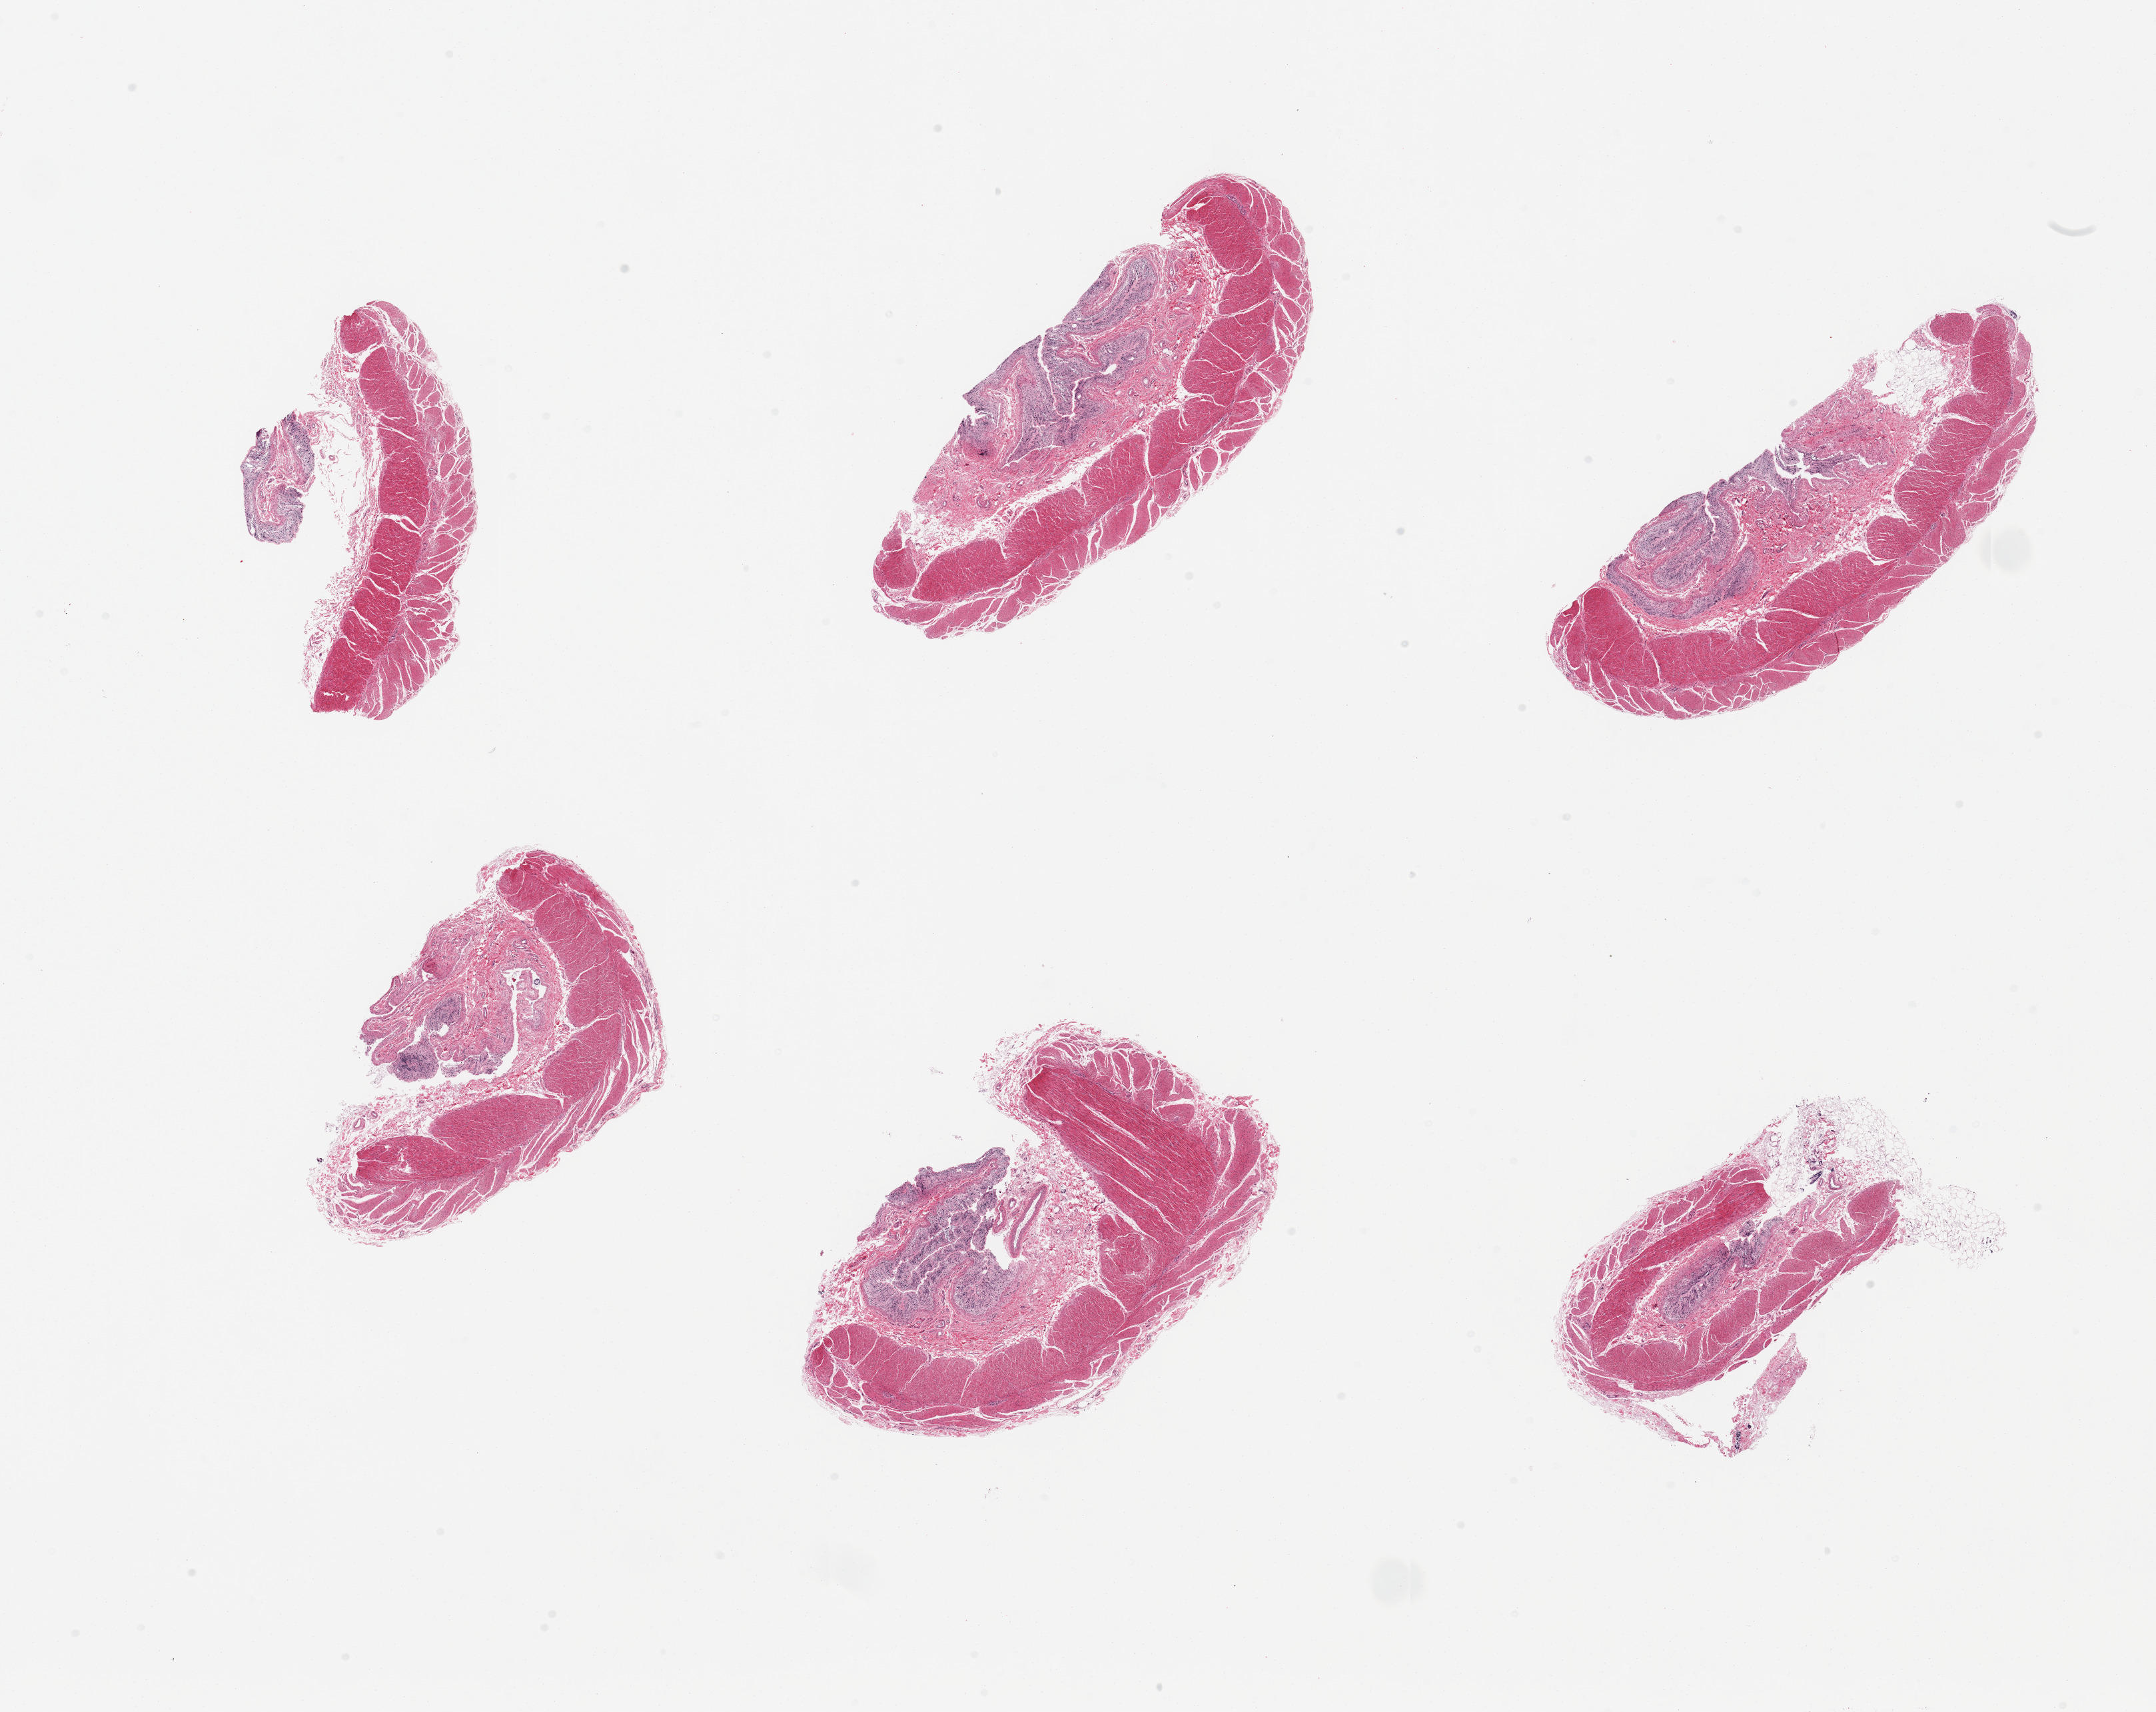
Hematoxylin and eosin (H&E) whole-slide image — whole scanned area (about 25.6 x 20.3 mm) shown as a low-resolution overview. PAXgene-fixed paraffin-embedded (PFPE) section. Section of ileum (target tissue). Donor tissue sample. Female donor.
Reviewer comment on this tissue sample: 6 pieces; autolyzed colonic mucosa (not target) and muscularis.